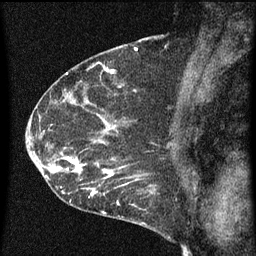
Breast MRI (dynamic contrast-enhanced), one sagittal slice. Position 41 of 60 along the scan axis. Dynamic contrast-enhanced series, image 2 of 3 at this slice position (ordered by acquisition). 1.5 T. TE 4.2 ms, TR 8 ms. 2 mm slice thickness. 256 × 256 image matrix, field of view 180 × 180 mm. Patient: female, 54 years.
Annotated regions visible in this slice (semi-automatic segmentation, software-assisted and operator-edited):
- analysis volume of interest (the breast-tissue region the enhancement analysis was run in; not a lesion): bounding box <49,138,163,209> (left, top, right, bottom; pixels)
- tumour enhancement mask (voxels above the 70 % enhancement threshold inside the analysis volume of interest): <49,142,156,209>